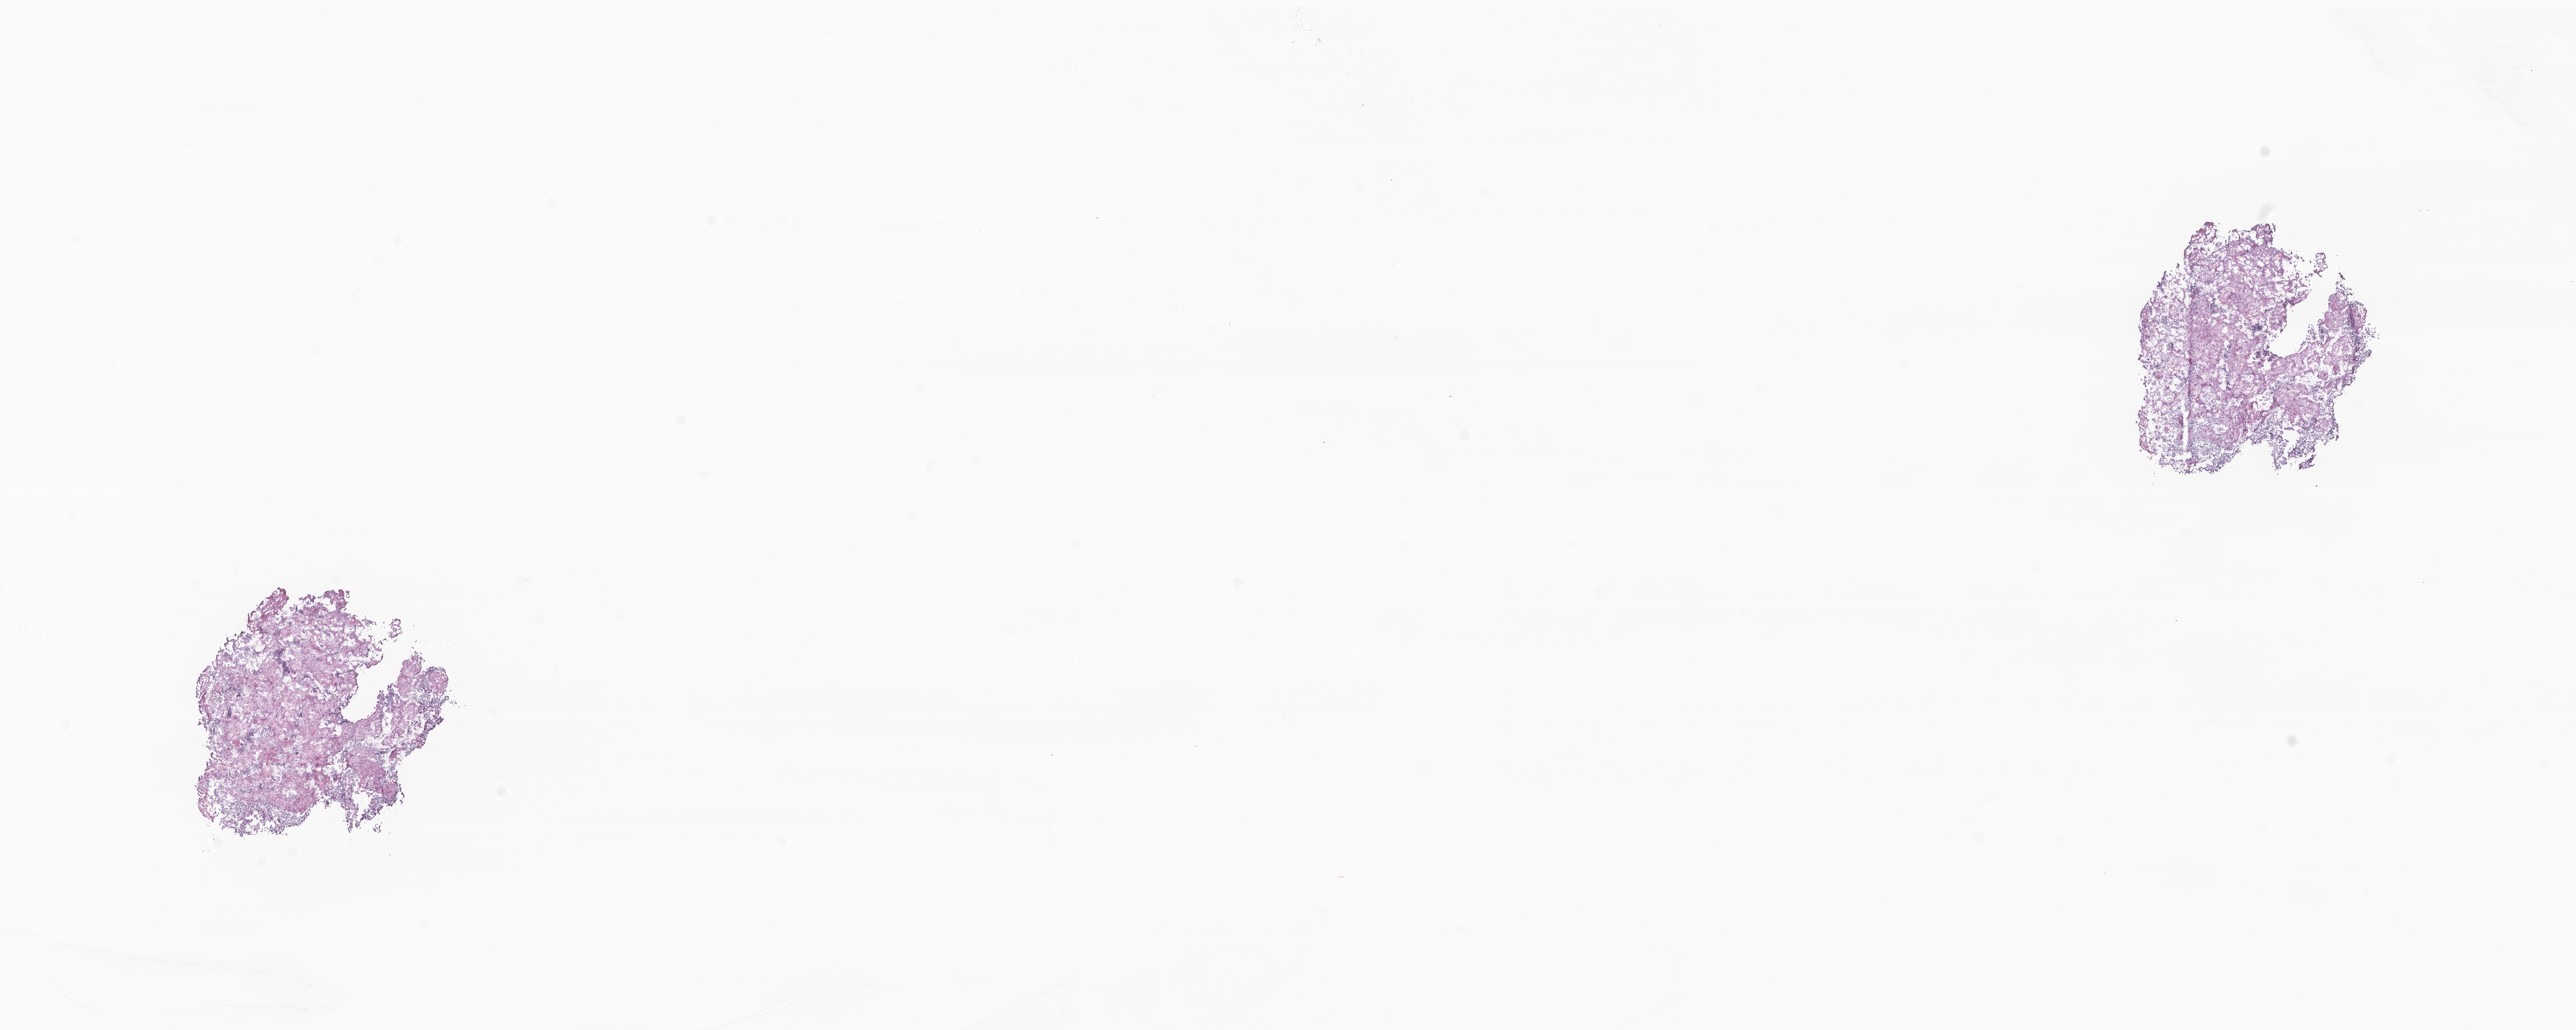
Whole-slide image, haematoxylin and eosin stain of tumor tissue from the brain stem, whole scanned area (about 24.5 x 9.8 mm) shown as a low-resolution overview; cryosection (OCT / tissue freezing medium). Female patient, age 107 months (8 years 11 months).
* diagnosis: Medulloblastoma, NOS